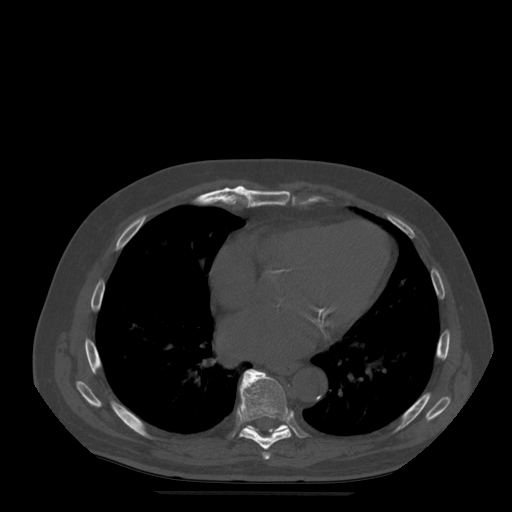
CT including the spine, one axial slice. Position 307 of 522 along the scan axis. Bone window (W 1800 / L 400 HU). 1.25 mm slice thickness. 512 × 512 image matrix. Patient age 72 years. Case-level facts recorded for this patient, not image findings: primary cancer: prostate.
Outlined on this slice (semi-automatic segmentation, software-assisted and operator-edited):
- T7 vertebra: bounding box (x1, y1, x2, y2) in pixels: (263, 452, 271, 460)
- T8 vertebra: (240, 370, 292, 450)
- T9 vertebra: (244, 369, 289, 434)